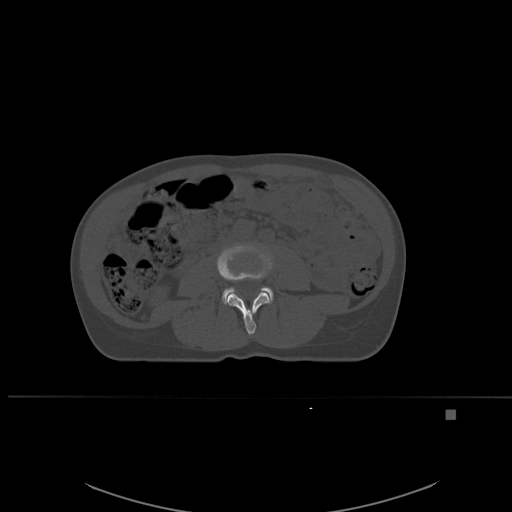
CT including the spine, one axial slice; position 205 of 537 along the scan axis; bone window (W 1800 / L 400 HU); 512 × 512 image matrix, field of view 440 × 440 mm. Female patient, age 45 years. From the clinical record (not read from this slice): primary cancer: lung.
Structures marked on this image (semi-automatically segmented with operator editing):
- L3 vertebra: bounding box <216,244,273,335> (left, top, right, bottom; pixels)
- L4 vertebra: <222,287,272,304>